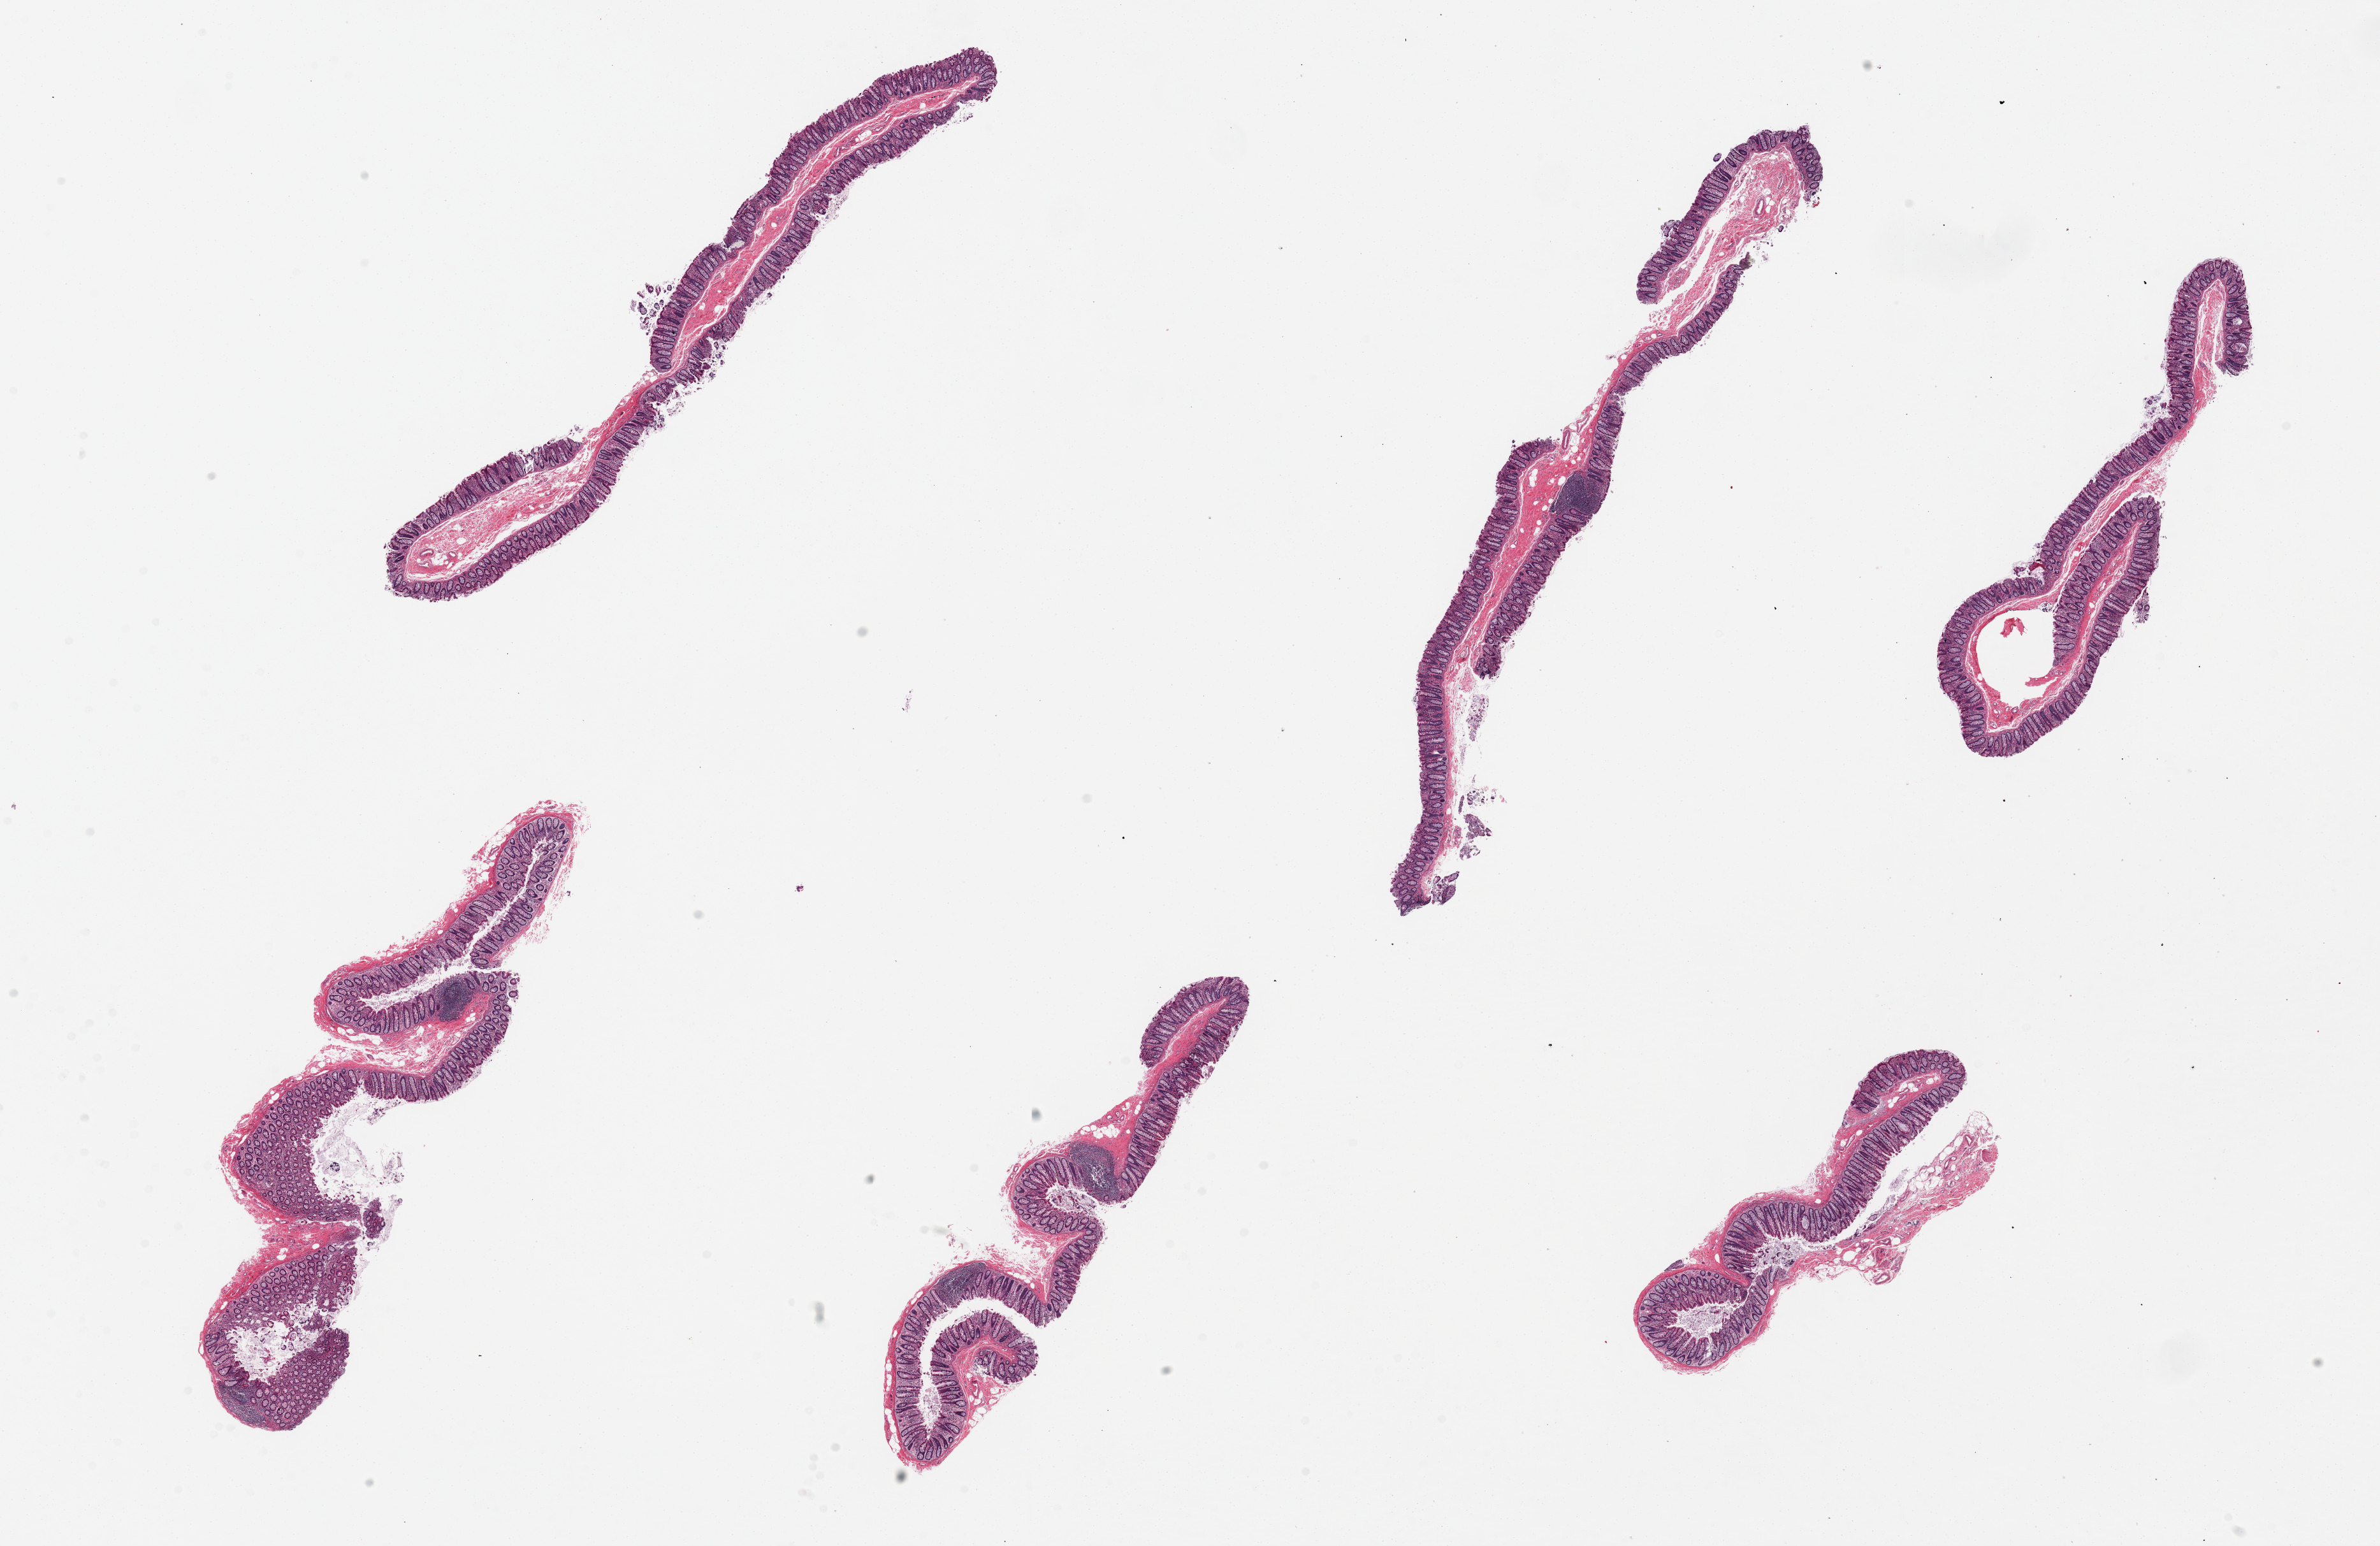
Hematoxylin and eosin (H&E) whole-slide image — whole scanned area (about 29.5 x 19.2 mm, slide scanned at 20x) shown as a low-resolution overview. PAXgene-fixed paraffin-embedded (PFPE) section. Section of transverse colon (target tissue). Tissue donor sample. Donor: female.
Review note (as recorded): 6 pieces, up to 11x2mm. All have only mucosa-submucosa; transverse colon should contain muscularis propria.